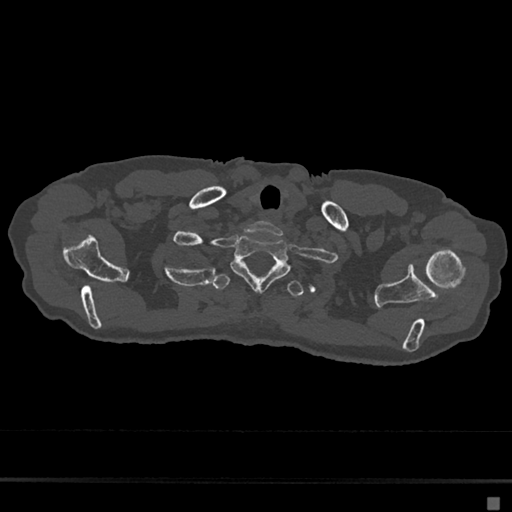
CT including the spine, one axial slice; position 603 of 797 along the scan axis; reconstruction kernel Br40s/3; 120 kVp; bone window (W 1800 / L 400 HU); 512 × 512 image matrix, field of view 360 × 360 mm. Female patient, age 68 years. Case-level facts recorded for this patient, not image findings: primary cancer: renal.
Structures marked on this image (semi-automatically segmented with operator editing):
- T1 vertebra: bounding box [x1, y1, x2, y2] px = [231, 235, 291, 291]
- T2 vertebra: [212, 274, 304, 298]